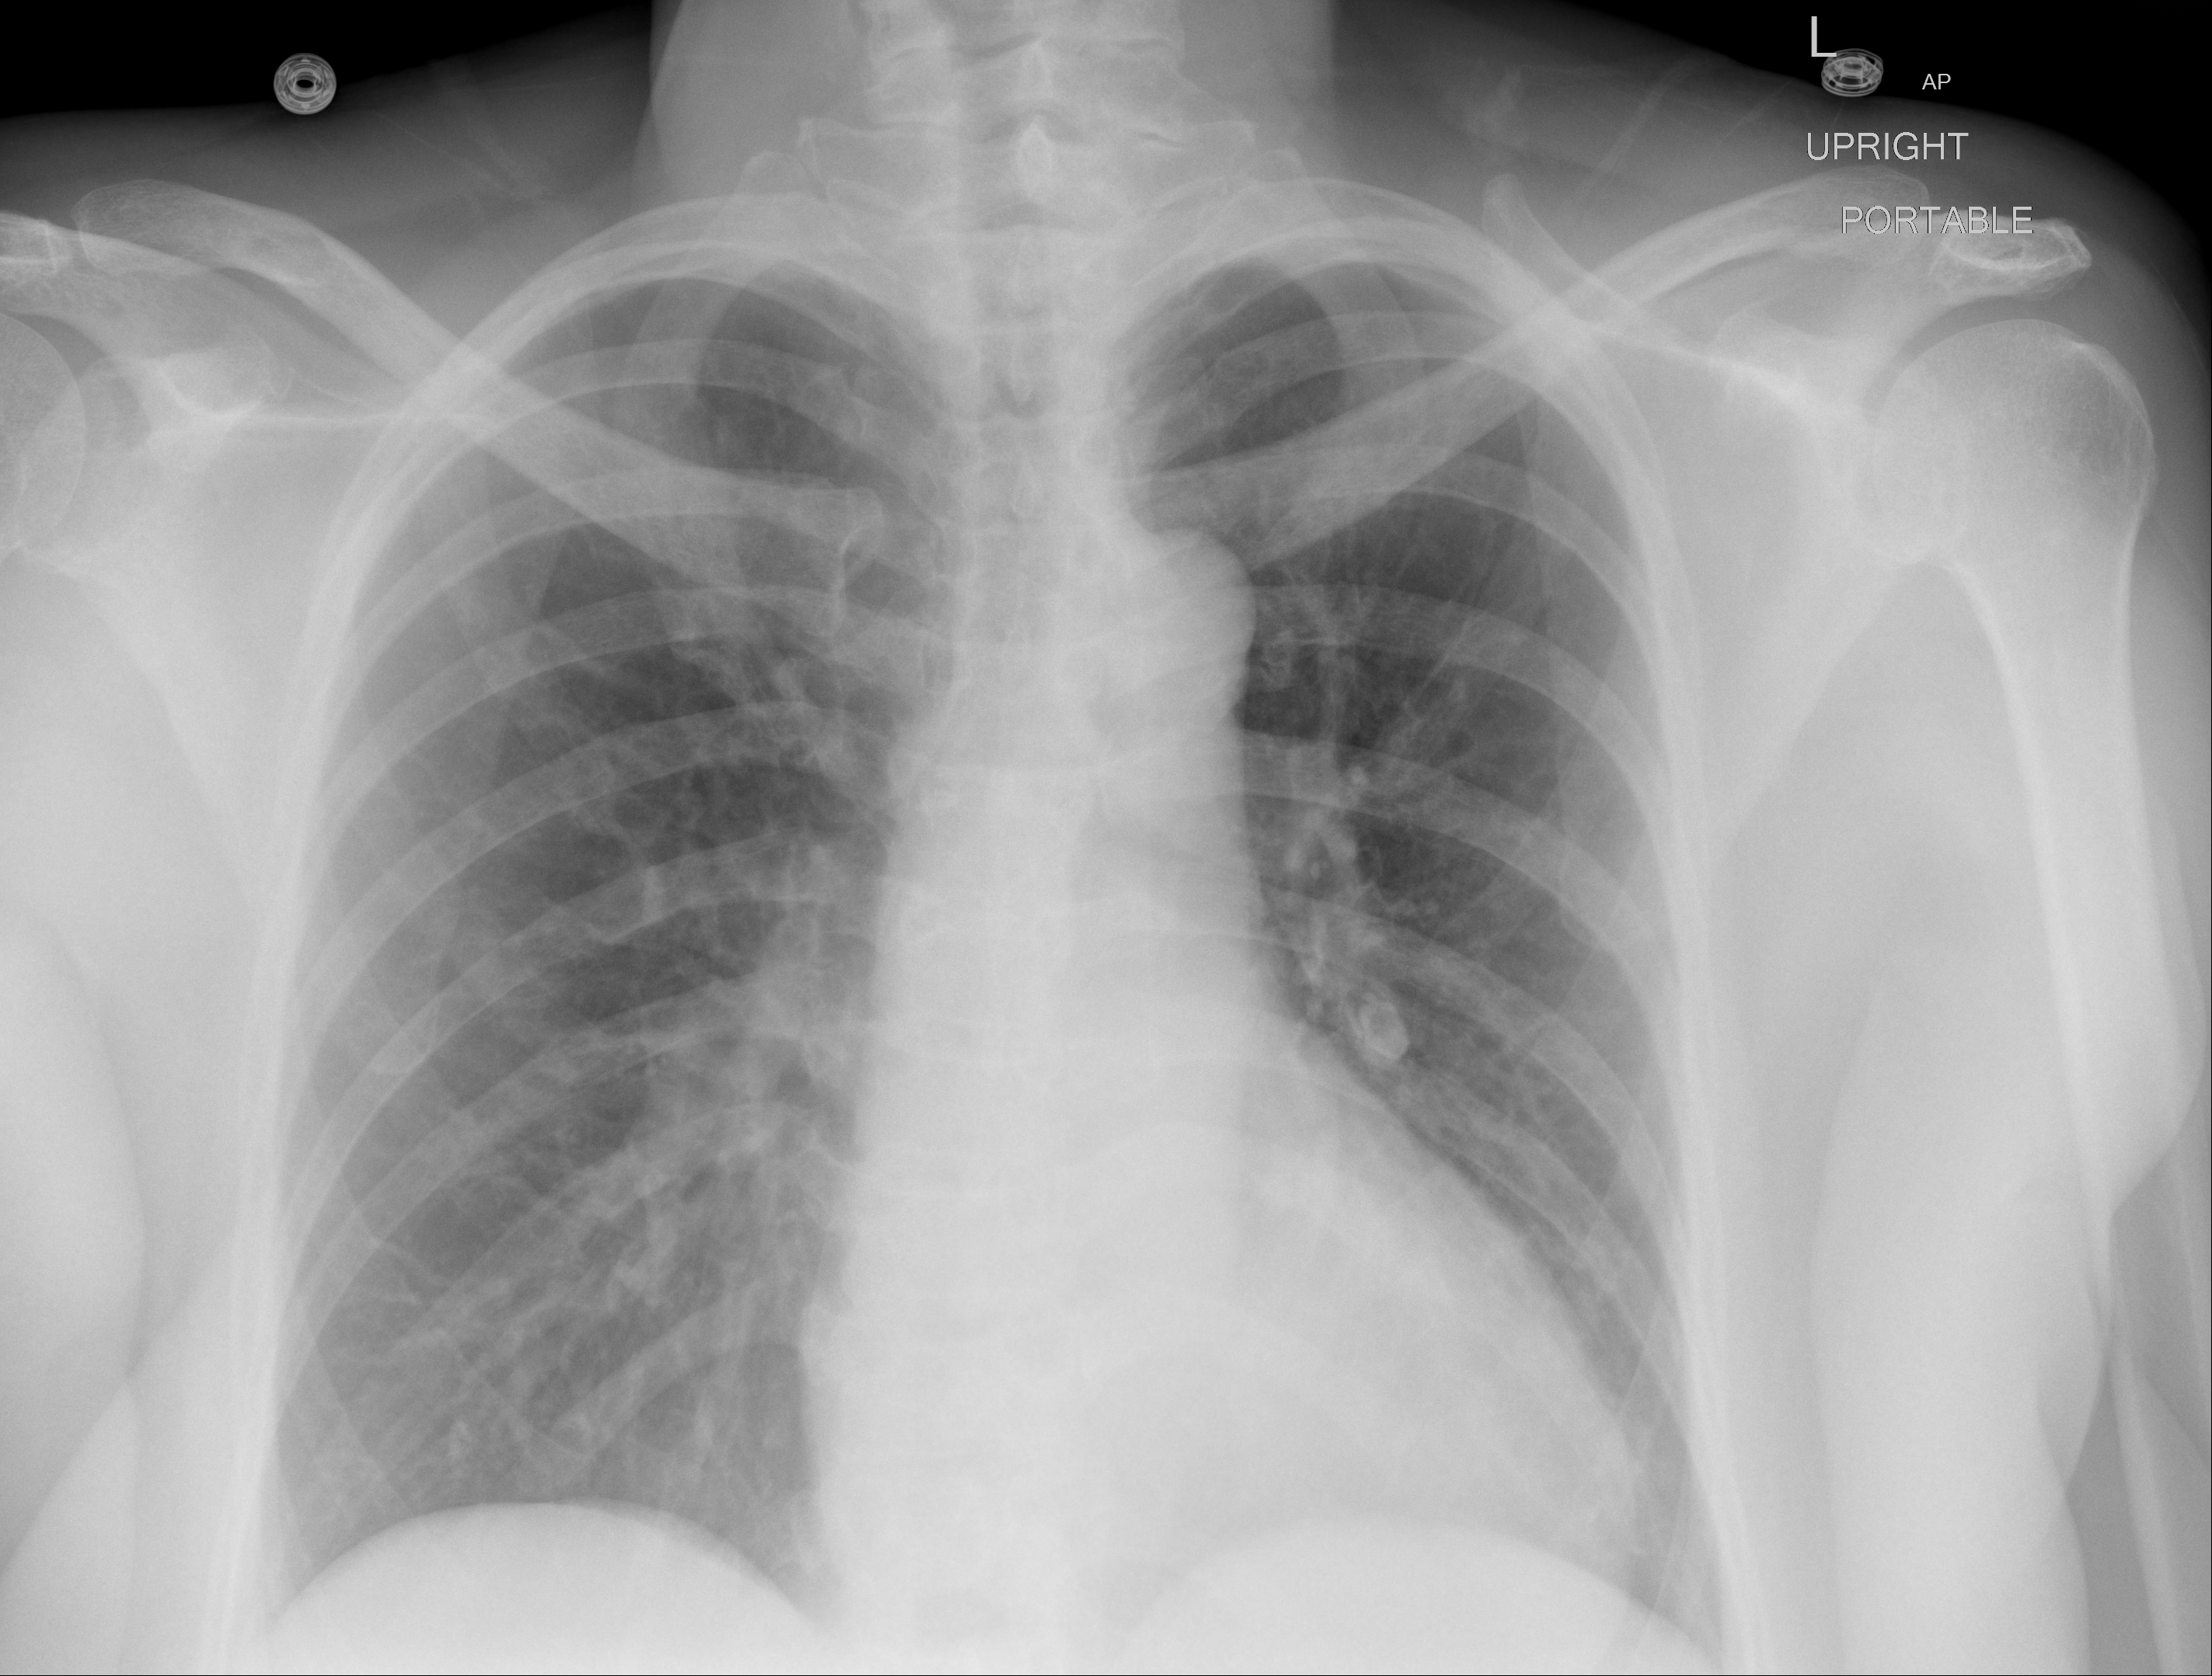
Portable chest radiograph, AP projection. Female patient, age 51 years; imaged 5 days after the COVID-19 diagnosis.
Key findings recorded by the radiologist: The lungs are clear without focal airspace opacification.